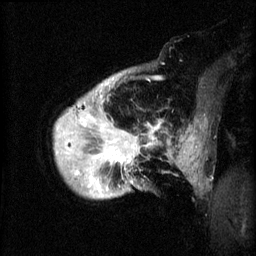
Breast MRI (dynamic contrast-enhanced), one sagittal slice. 3 images stored at this slice position (order not interpretable as contrast timing). 1.5 T. TE 4.2 ms, TR 8.2 ms. 2 mm slice thickness. 256 × 256 image matrix, field of view 200 × 200 mm. Female patient, age 50 years.
Structures marked on this image (semi-automatically segmented with operator editing):
- analysis volume of interest (the breast-tissue region the enhancement analysis was run in; not a lesion): bounding box <54,72,170,199> (left, top, right, bottom; pixels)
- tumour enhancement mask (voxels above the 70 % enhancement threshold inside the analysis volume of interest): <76,110,163,191>